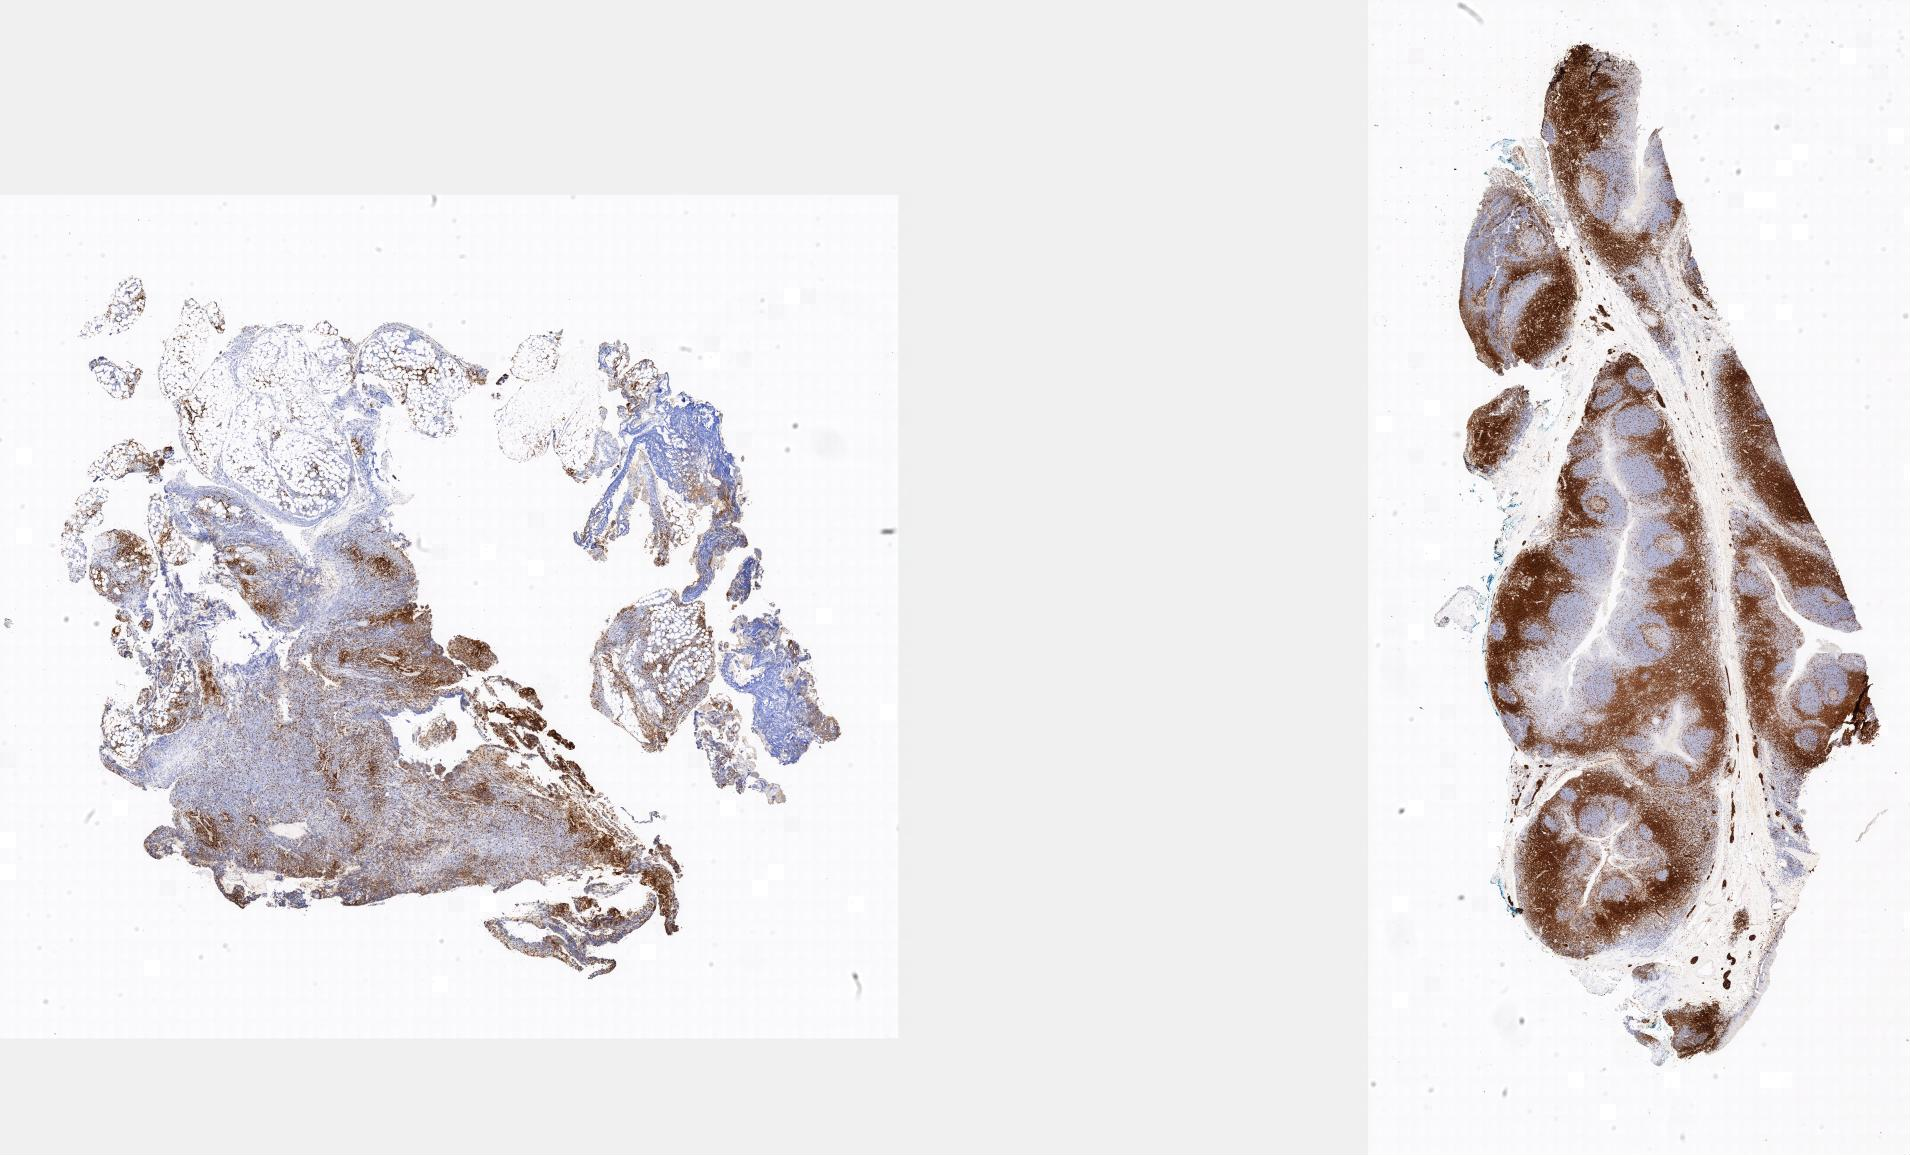
Immunohistochemistry (IHC) whole-slide image stained for CD3, whole scanned area shown as a low-resolution overview; specimen: tumor tissue; site: abdominal lymph node. Patient: male, age at initial diagnosis 9 years.
Histologic diagnosis: Burkitt lymphoma, NOS.